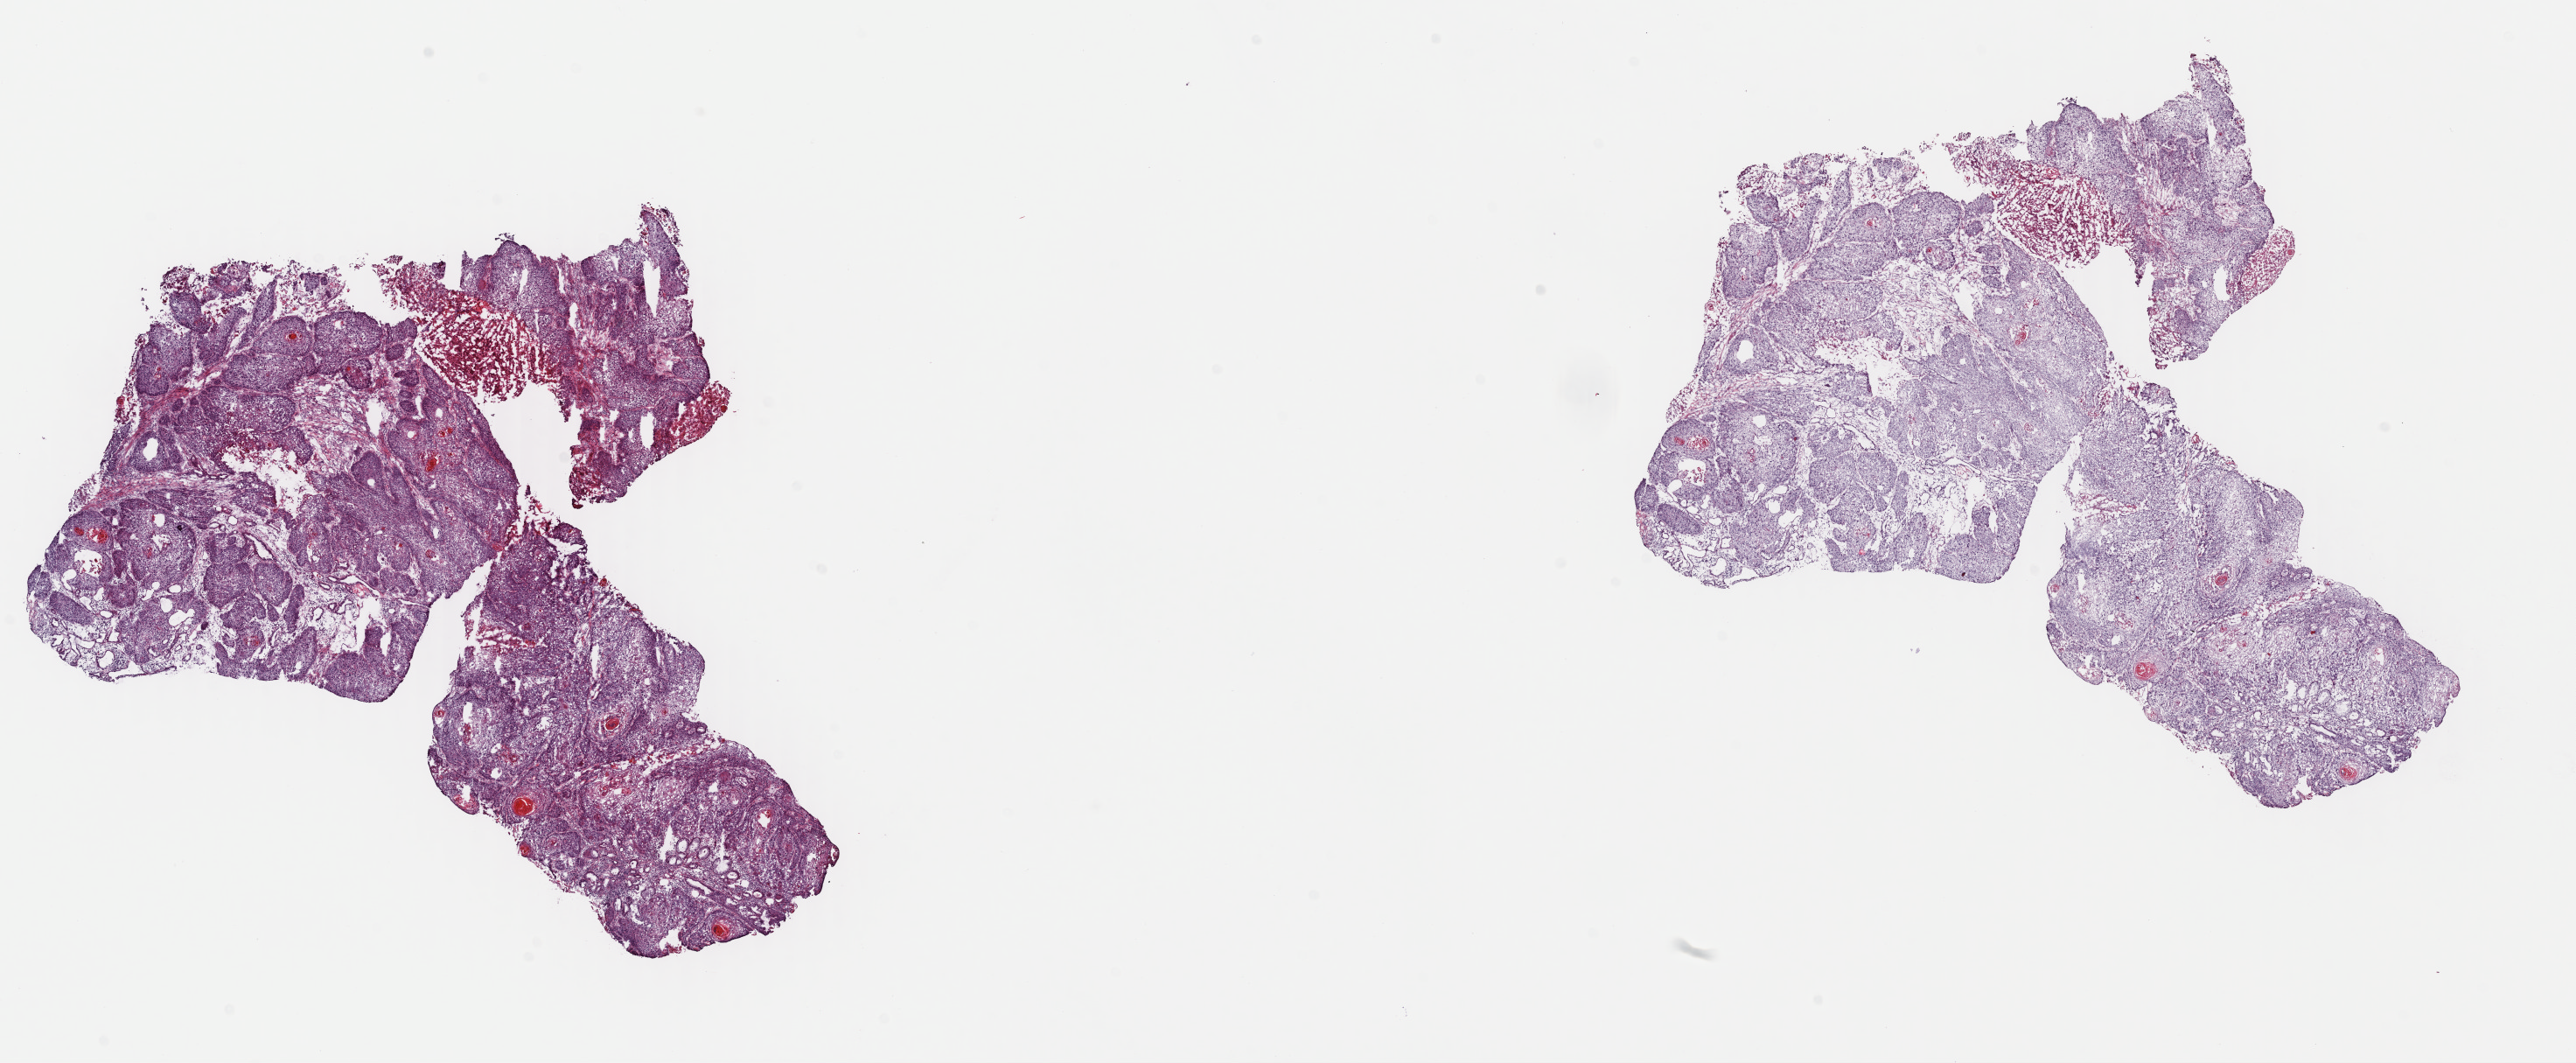
Whole-slide histology image, H&E-stained, whole scanned area (about 23.1 x 9.5 mm, acquisition: 40x scan) shown as a low-resolution overview, frozen section from the top of the tissue portion, head and neck, primary tumour sample. Female, age 48 years at initial diagnosis. Histologic grade: G2 (moderately differentiated). Slide review estimates, as recorded: tumour cells 80%, tumour nuclei 80%, normal cells 0%, stromal cells 10%, necrosis 10%. Inflammatory infiltration, as recorded: lymphocyte infiltration 40%, monocyte infiltration 20%, neutrophil infiltration 20%.
Lymph nodes positive (case pathology): 0 of 66 examined. Diagnosis: Squamous cell carcinoma, NOS (larynx, NOS). AJCC pathologic stage: IVA (7th edition).